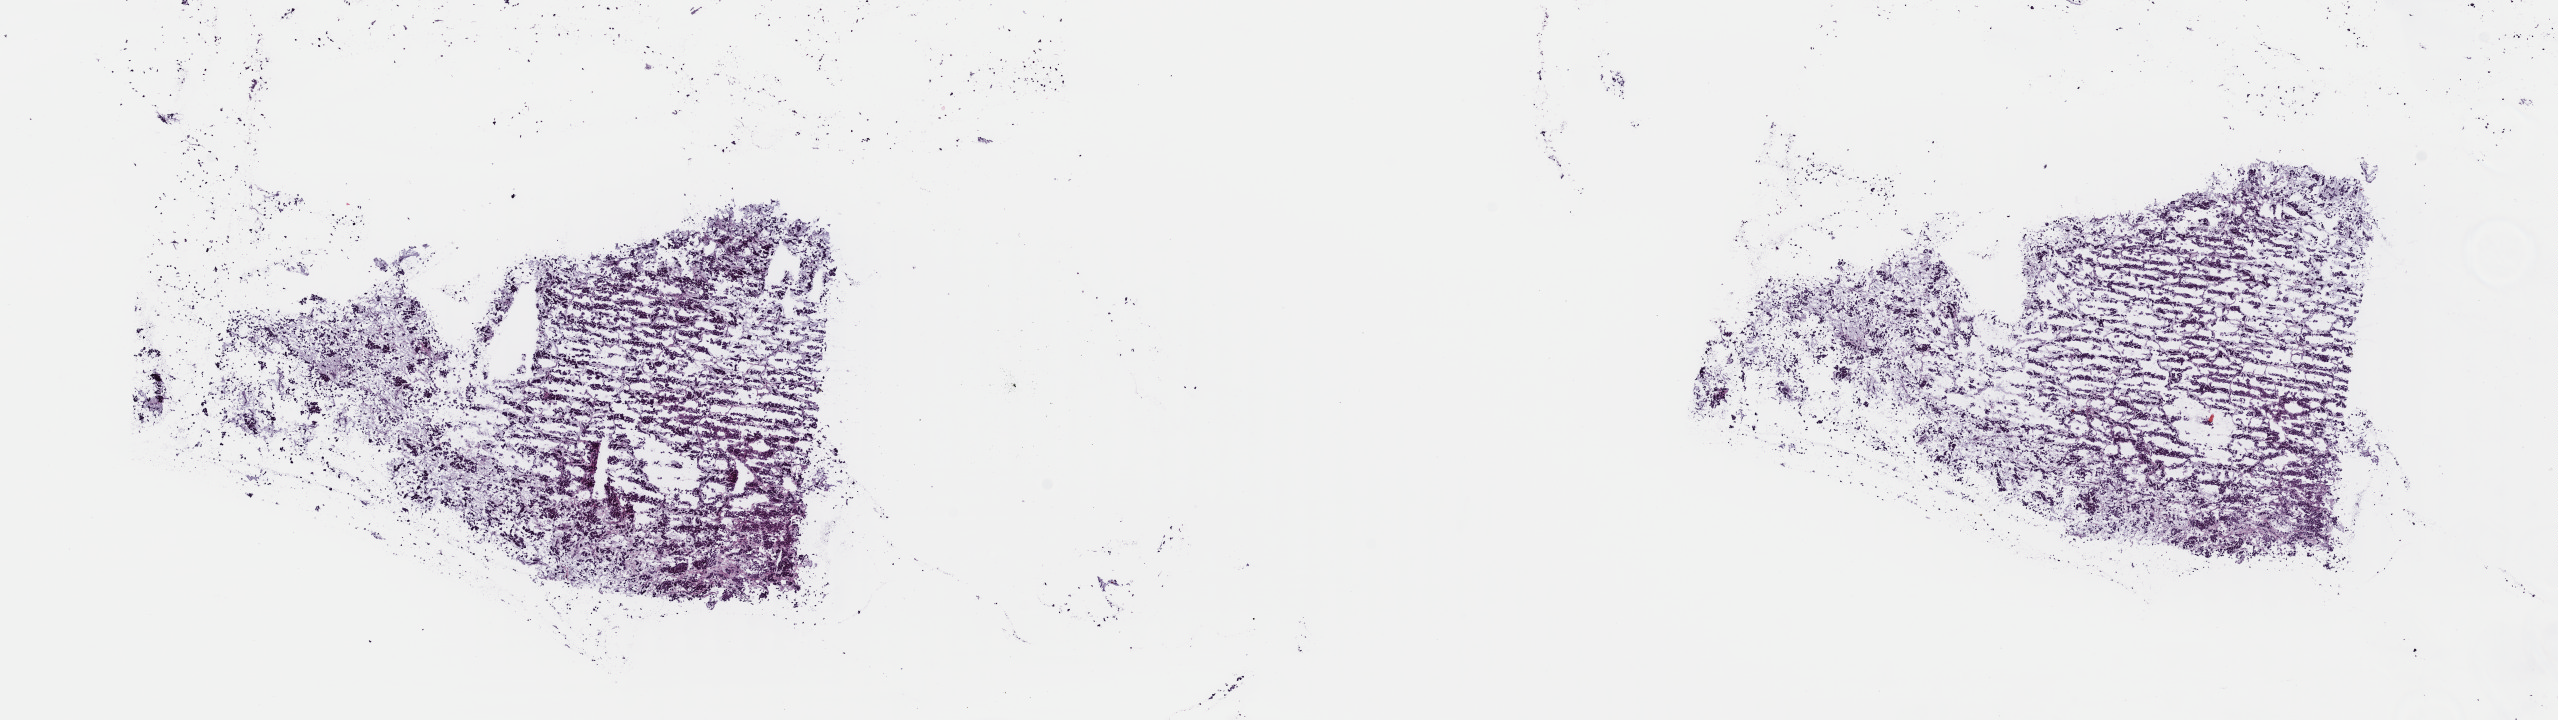
H&E whole-slide image — shown as a low-resolution overview of the whole scanned area (about 20.2 x 5.7 mm, acquisition: 40x scan), frozen section, adrenal cortex, primary tumour sample. Female patient; age at initial diagnosis 37 years. Pathologist review of this section (percent, as recorded): tumour cells 80%, tumour nuclei 90%, normal cells 0%, stromal cells 20%, necrosis 0%. Infiltration values recorded for this section: lymphocyte infiltration 0%, monocyte infiltration 0%, neutrophil infiltration 0%.
Pathologic diagnosis: Adrenal cortical carcinoma (cortex of adrenal gland).